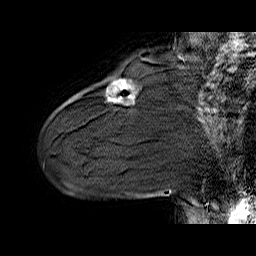
Breast MRI (dynamic contrast-enhanced), one sagittal slice; slice 14 of 60 in the series (ordered by position); dynamic contrast-enhanced series, time point 2 of 6 at this slice position (early post-contrast); 1.5 T; TE 6.4 ms, TR 32.9 ms; 256 × 256 image matrix, field of view 200 × 200 mm. Female patient. Case-level facts recorded for this patient, not image findings: setting: breast cancer imaged before/during neoadjuvant chemotherapy; receptor status: HER2-positive.
Structures marked on this image (semi-automatically segmented with operator editing):
- analysis volume of interest (the breast-tissue region the enhancement analysis was run in; not a lesion): bounding box <105,79,138,106> (left, top, right, bottom; pixels)
- tumour enhancement mask (voxels above the 100 % enhancement threshold inside the analysis volume of interest): <109,80,124,102>